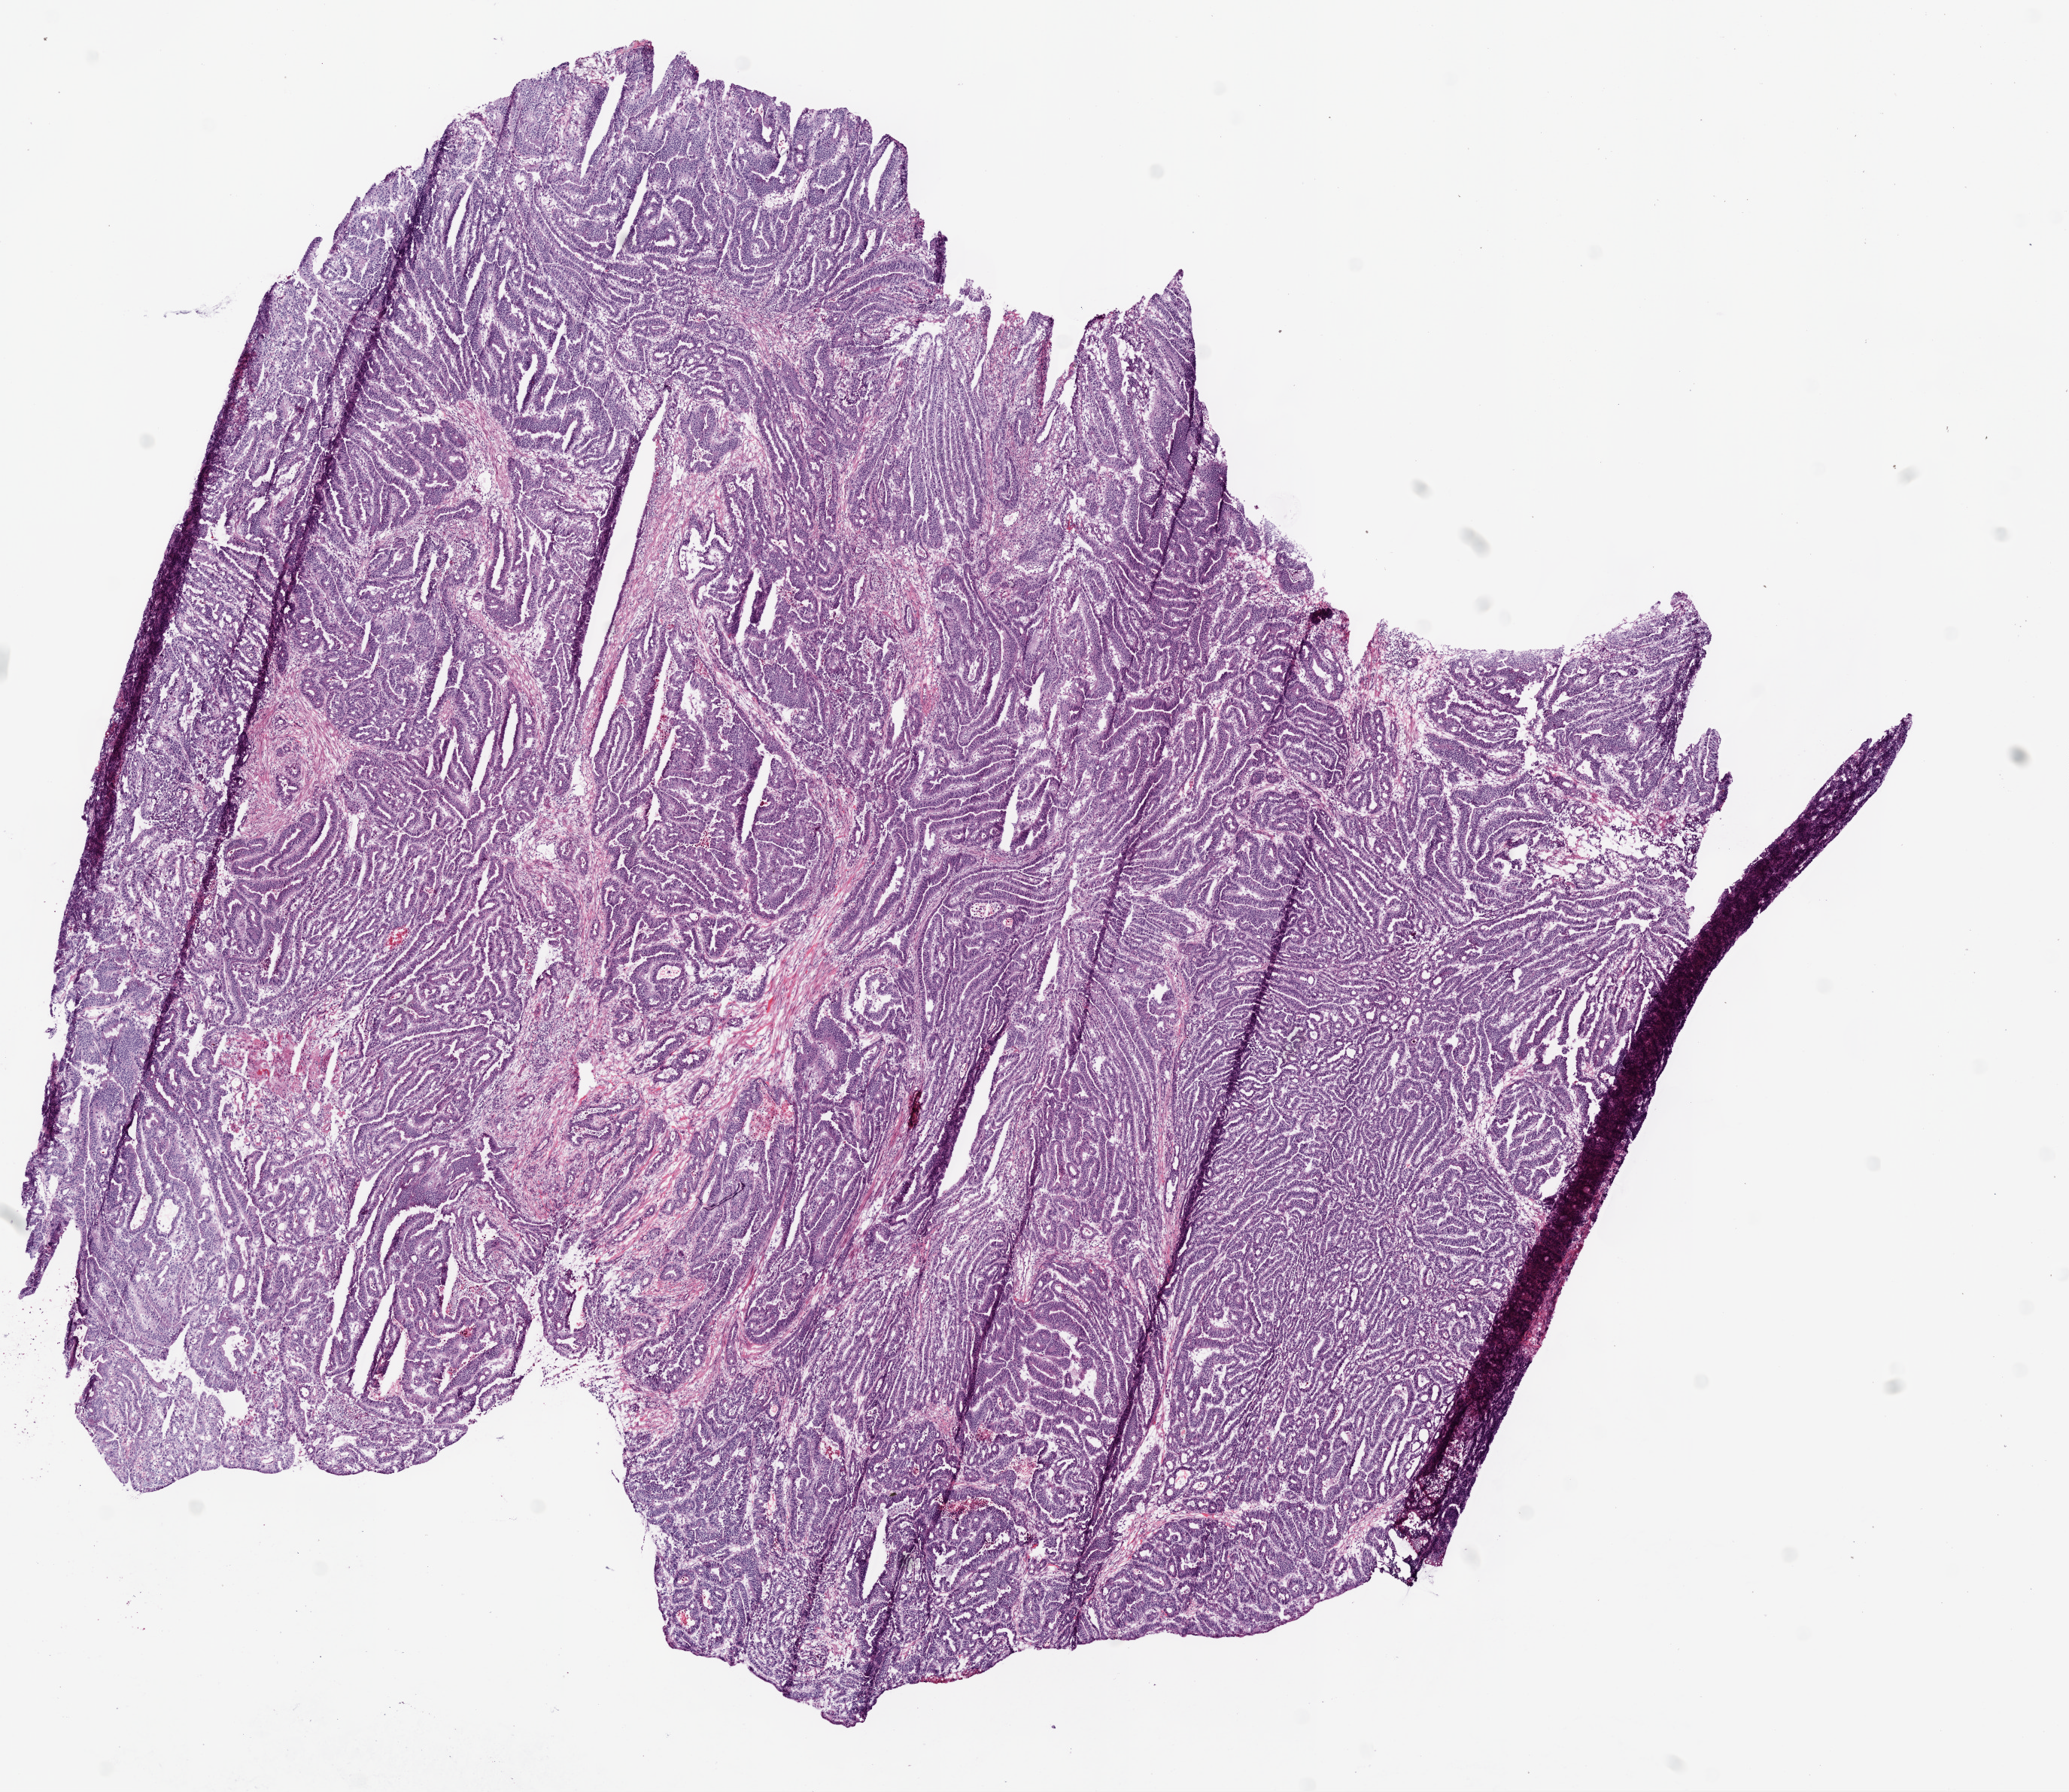
Digitized H&E tissue section (whole slide), low-resolution overview of the scanned area, about 11.0 x 9.6 mm (acquisition: 20x scan); frozen section; sample: primary tumour, colon. Male, age 68 years at initial diagnosis. Composition of this section per pathologist review: tumour cells 95%, tumour nuclei 80%, normal cells 0%, stromal cells 0%, necrosis 5%.
Lymph nodes positive (case pathology): 2 of 41 examined. AJCC pathologic stage: III. Pathologic diagnosis: Adenocarcinoma, NOS.